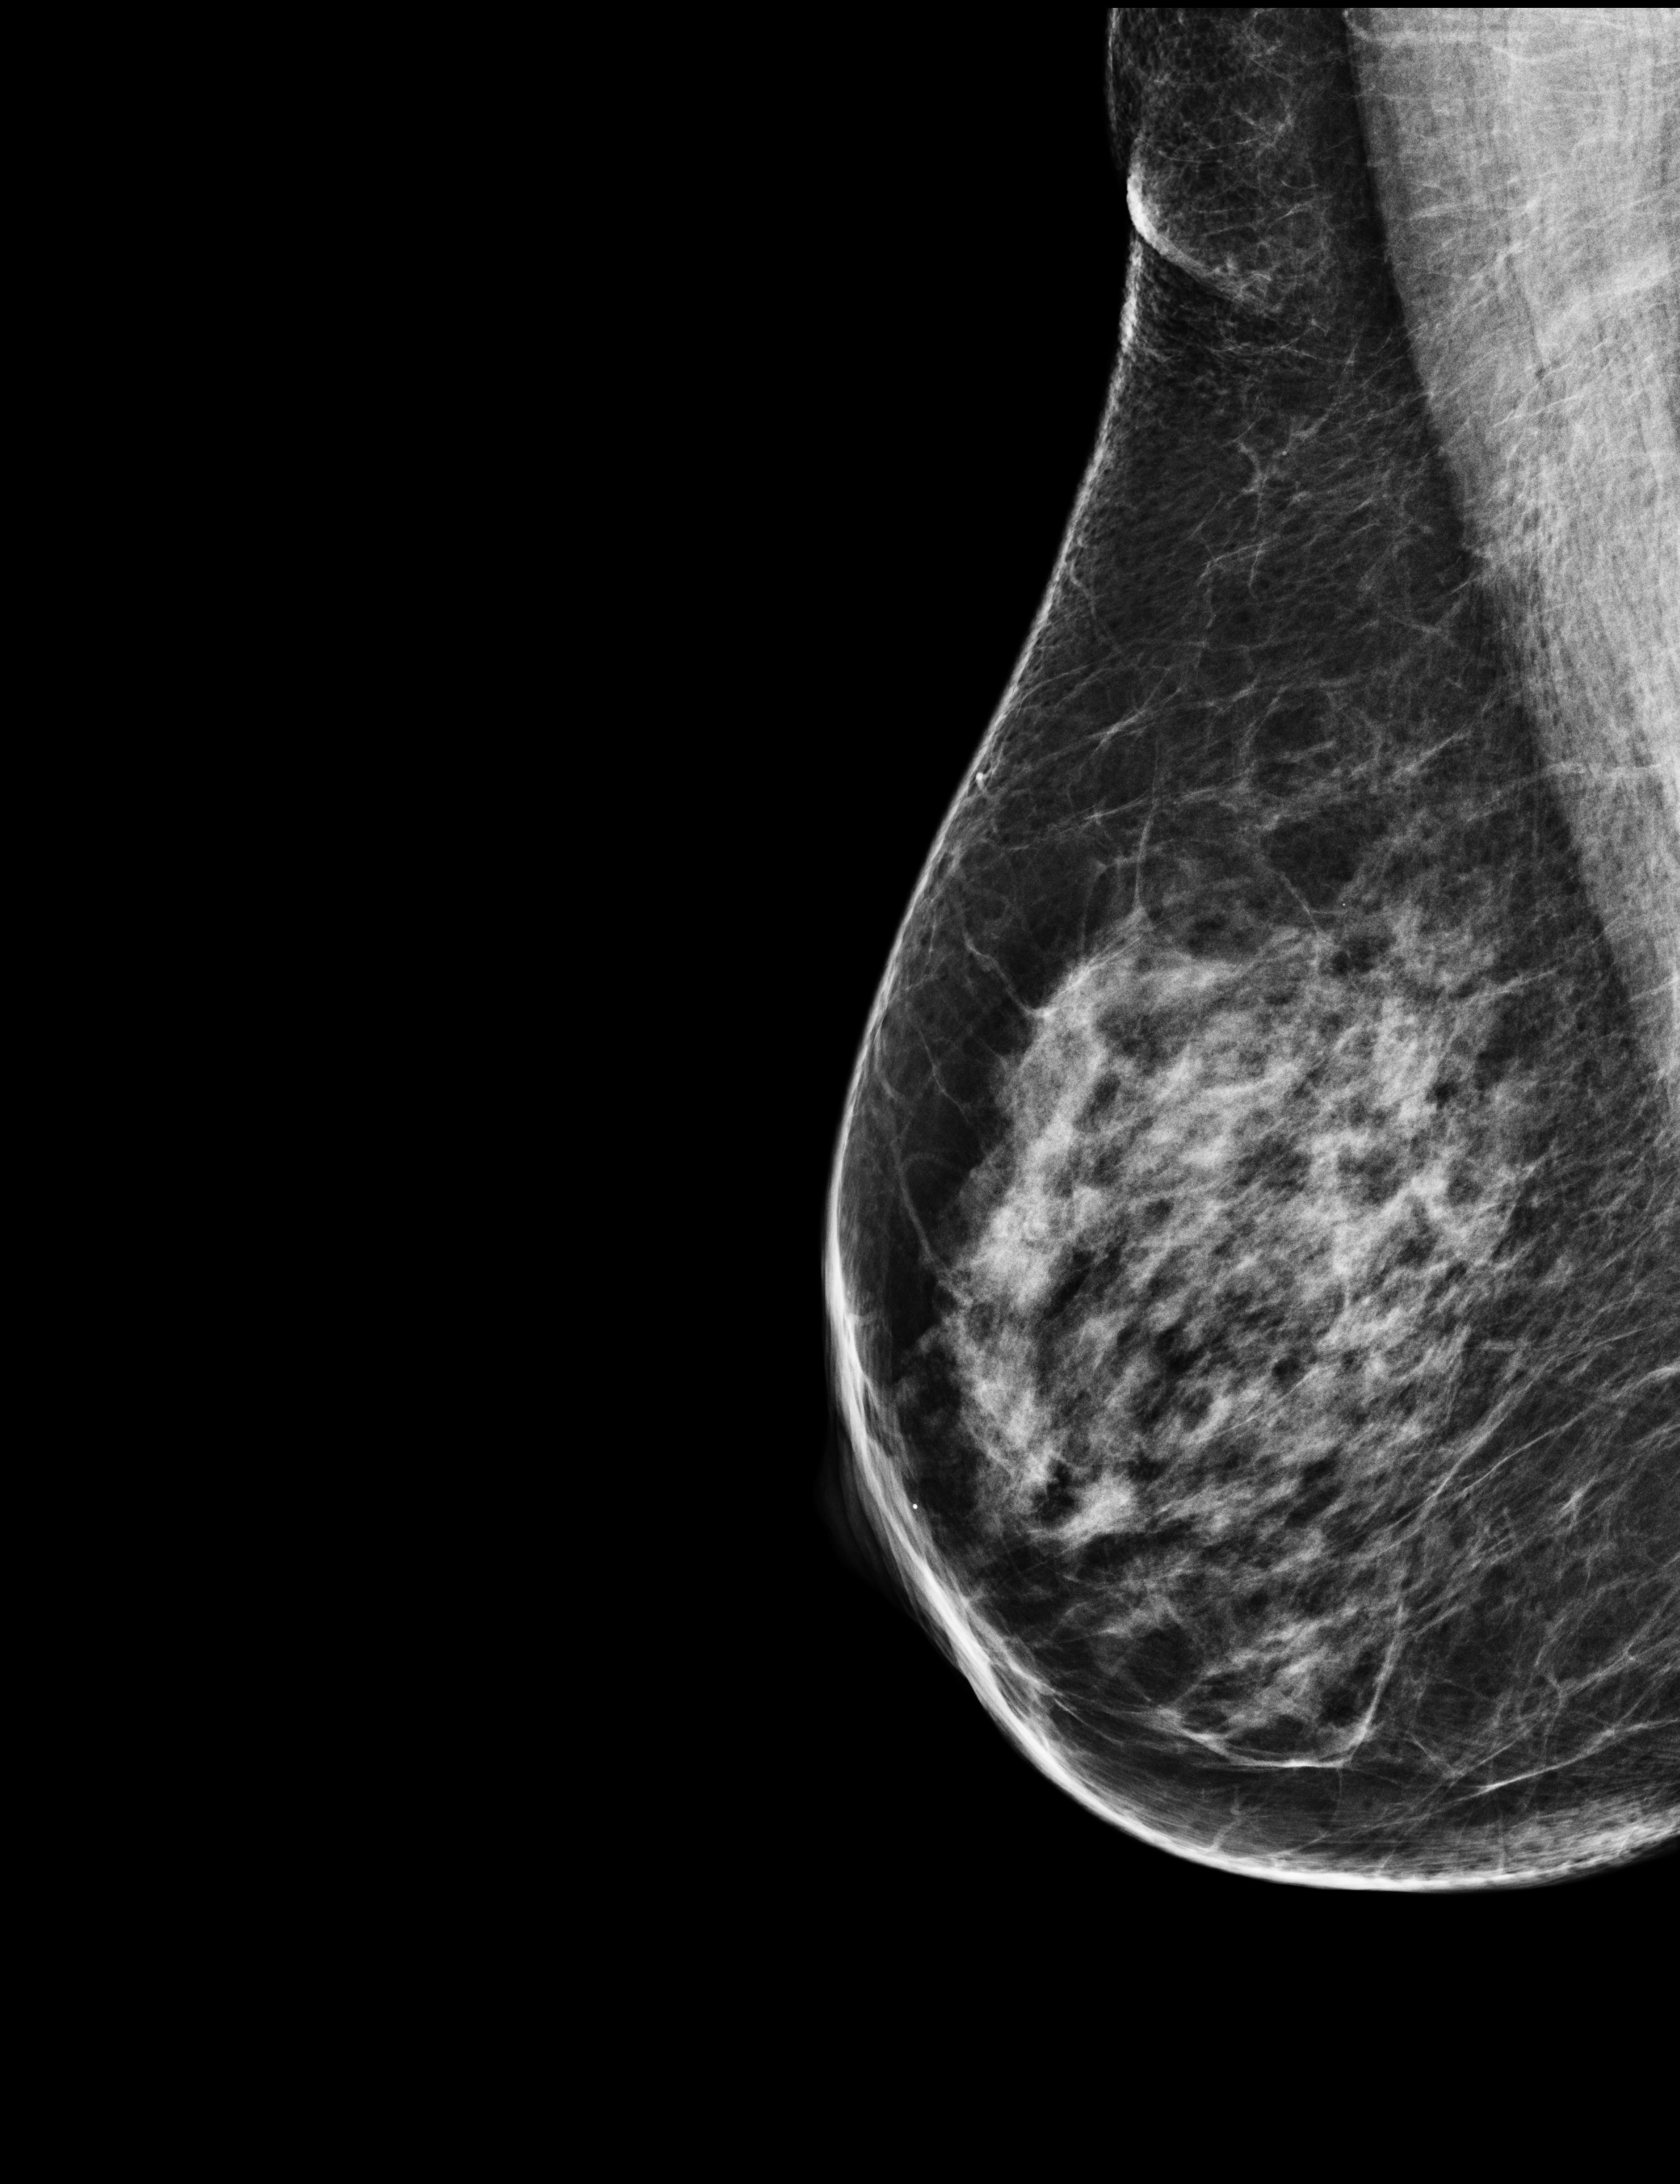
Annual screening mammography examination, system: Selenia Dimensions. Patient aged 61 years (female).
Image type: full-field digital mammogram. Breast: right. Projection: mediolateral oblique (MLO) view.